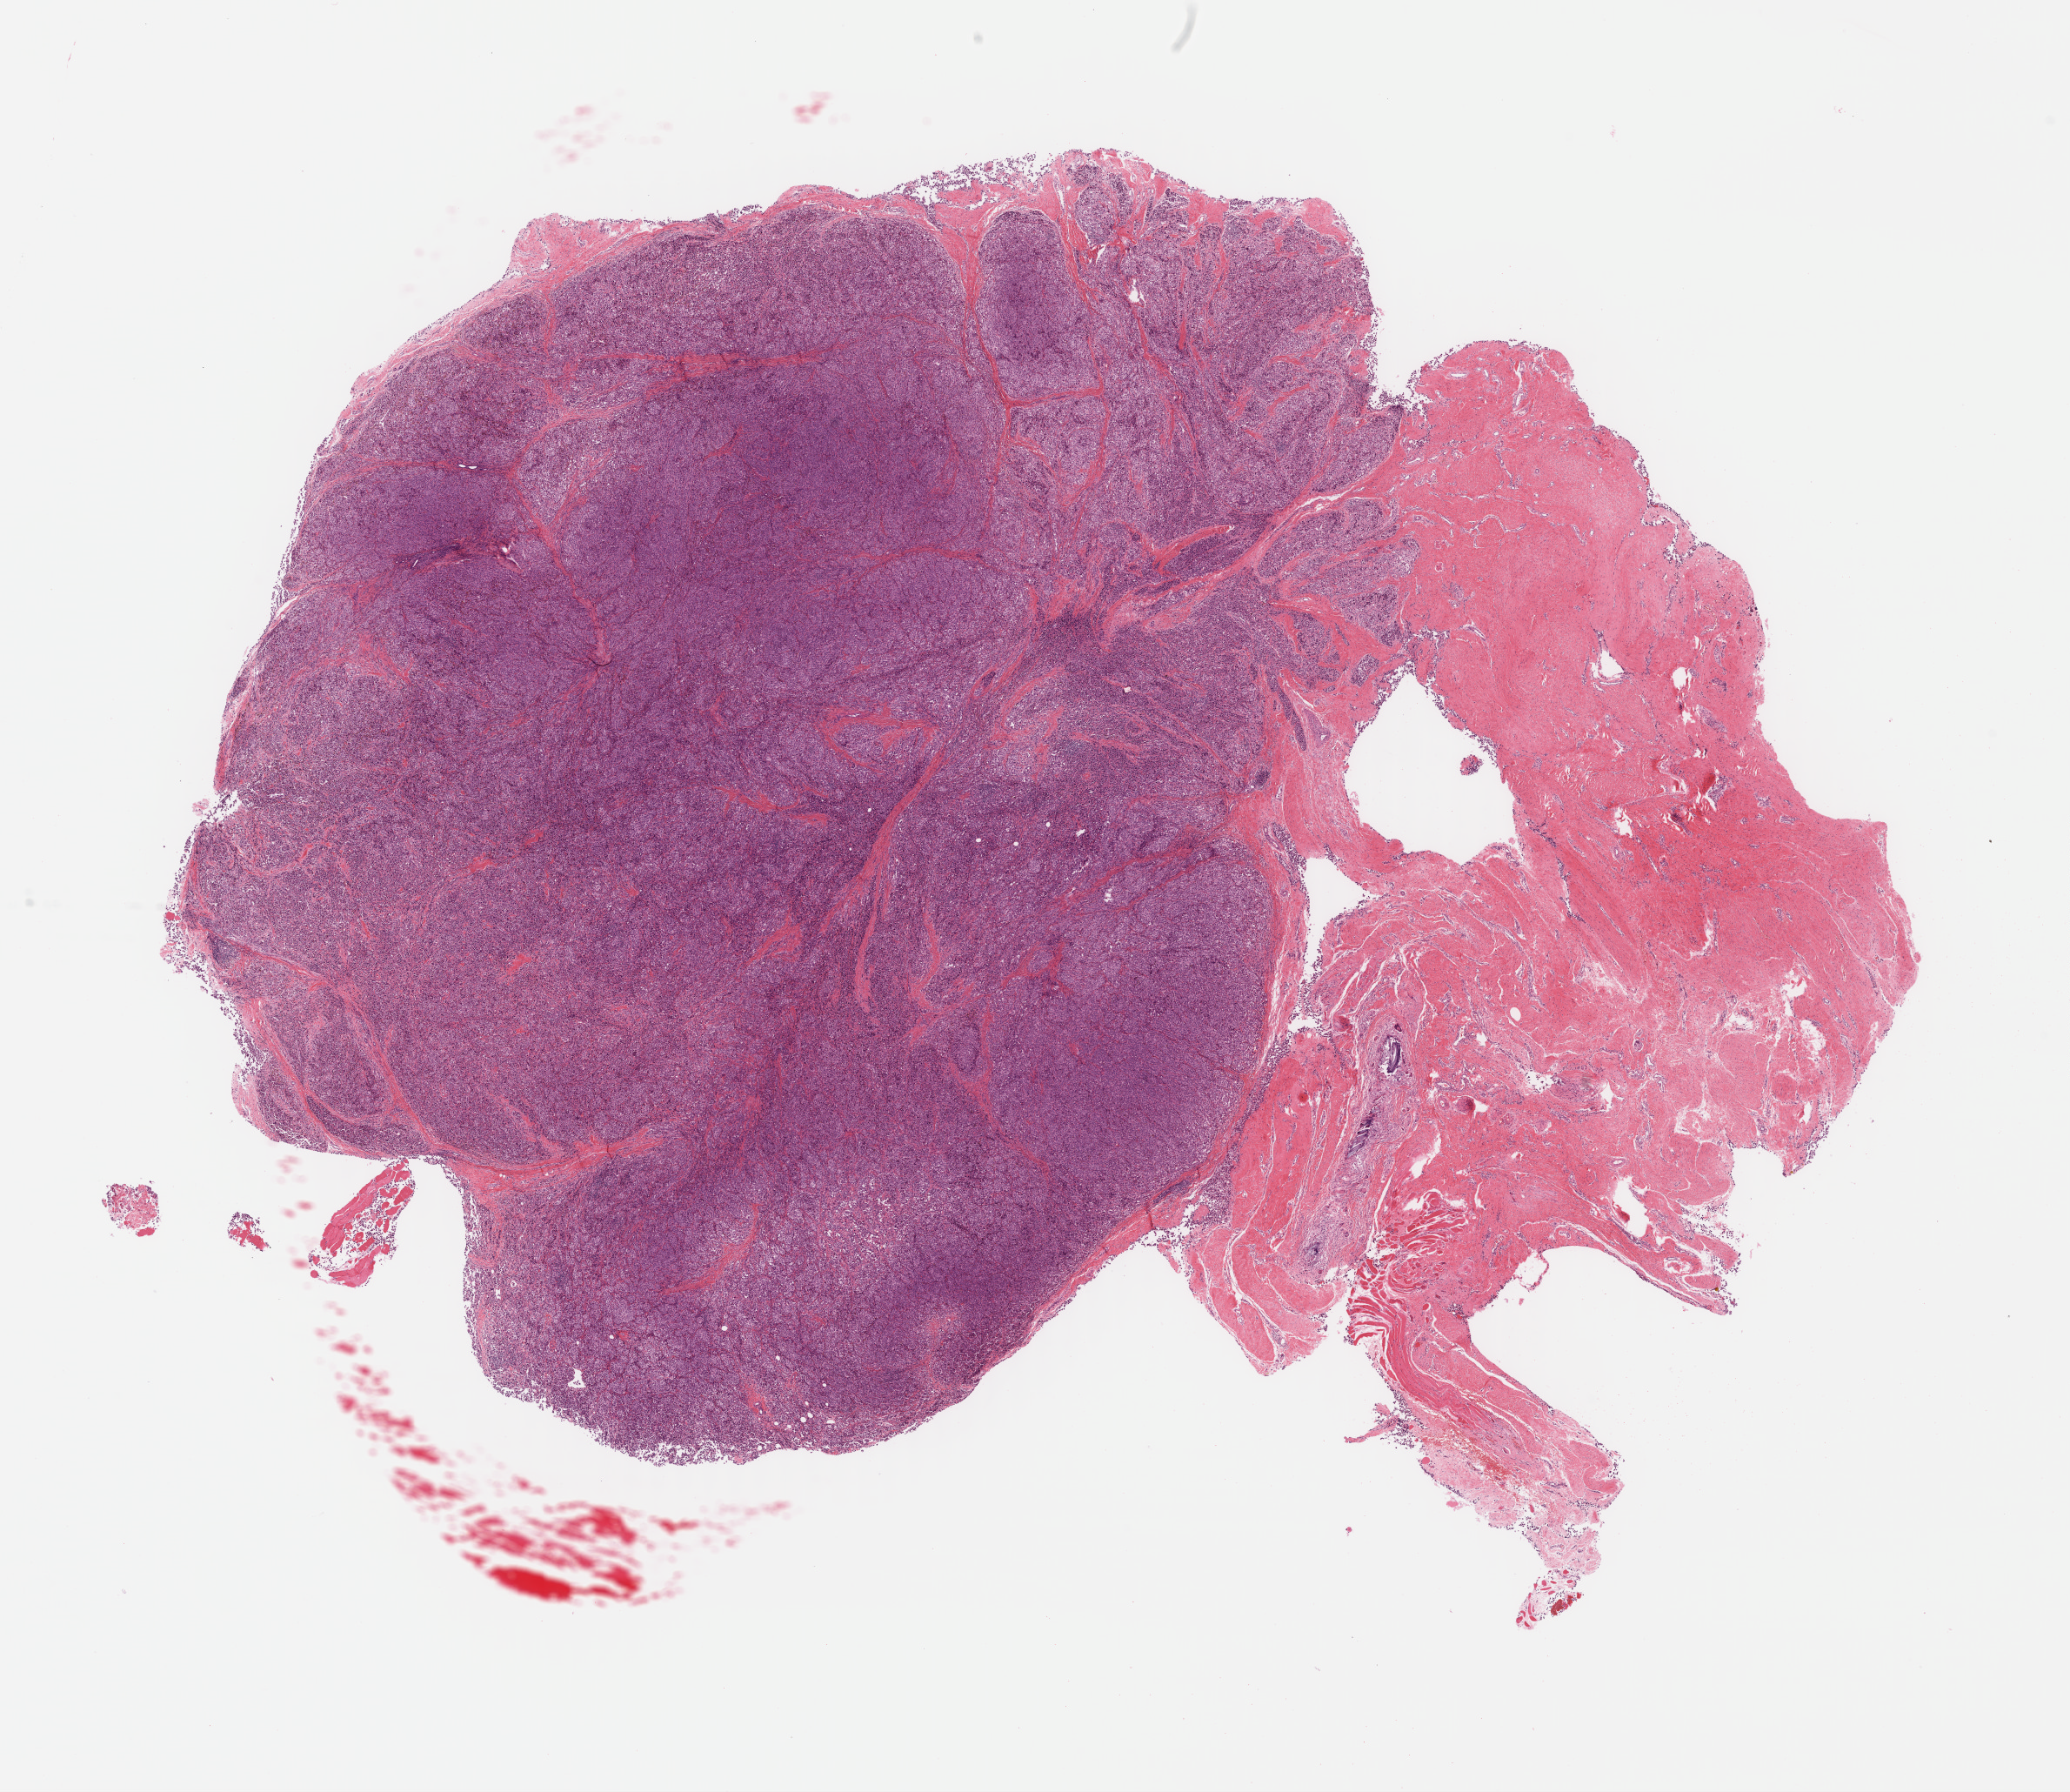
Digitized H&E tissue section (whole slide) — low-resolution overview of the scanned area, about 18.7 x 16.2 mm (slide scanned at 40x), formalin-fixed paraffin-embedded (FFPE) diagnostic section, sample: primary tumour, skin. Patient: male, age at initial diagnosis 52 years.
Histologic diagnosis: Malignant melanoma, NOS.